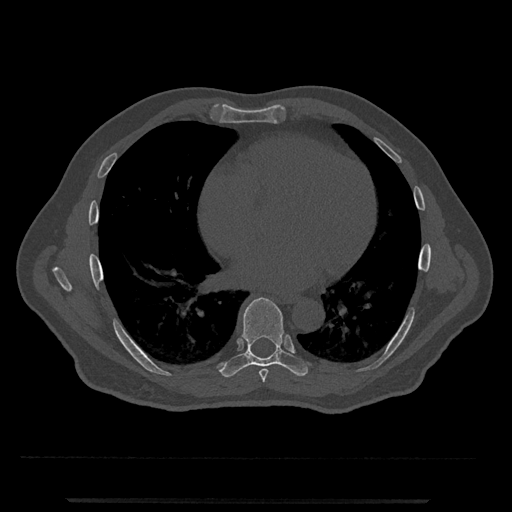
CT including the spine, one axial slice; slice 640 of 797 in the series (ordered by position); 120 kVp; bone window (W 1800 / L 400 HU); 0.5 mm slice thickness; 512 × 512 image matrix, field of view 419 × 419 mm. Male patient, age 63 years. From the clinical record (not read from this slice): primary cancer: prostate.
Structures marked on this image (semi-automatically segmented with operator editing):
- T7 vertebra: bounding box [x1, y1, x2, y2] px = [259, 369, 268, 382]
- T8 vertebra: [219, 297, 309, 377]